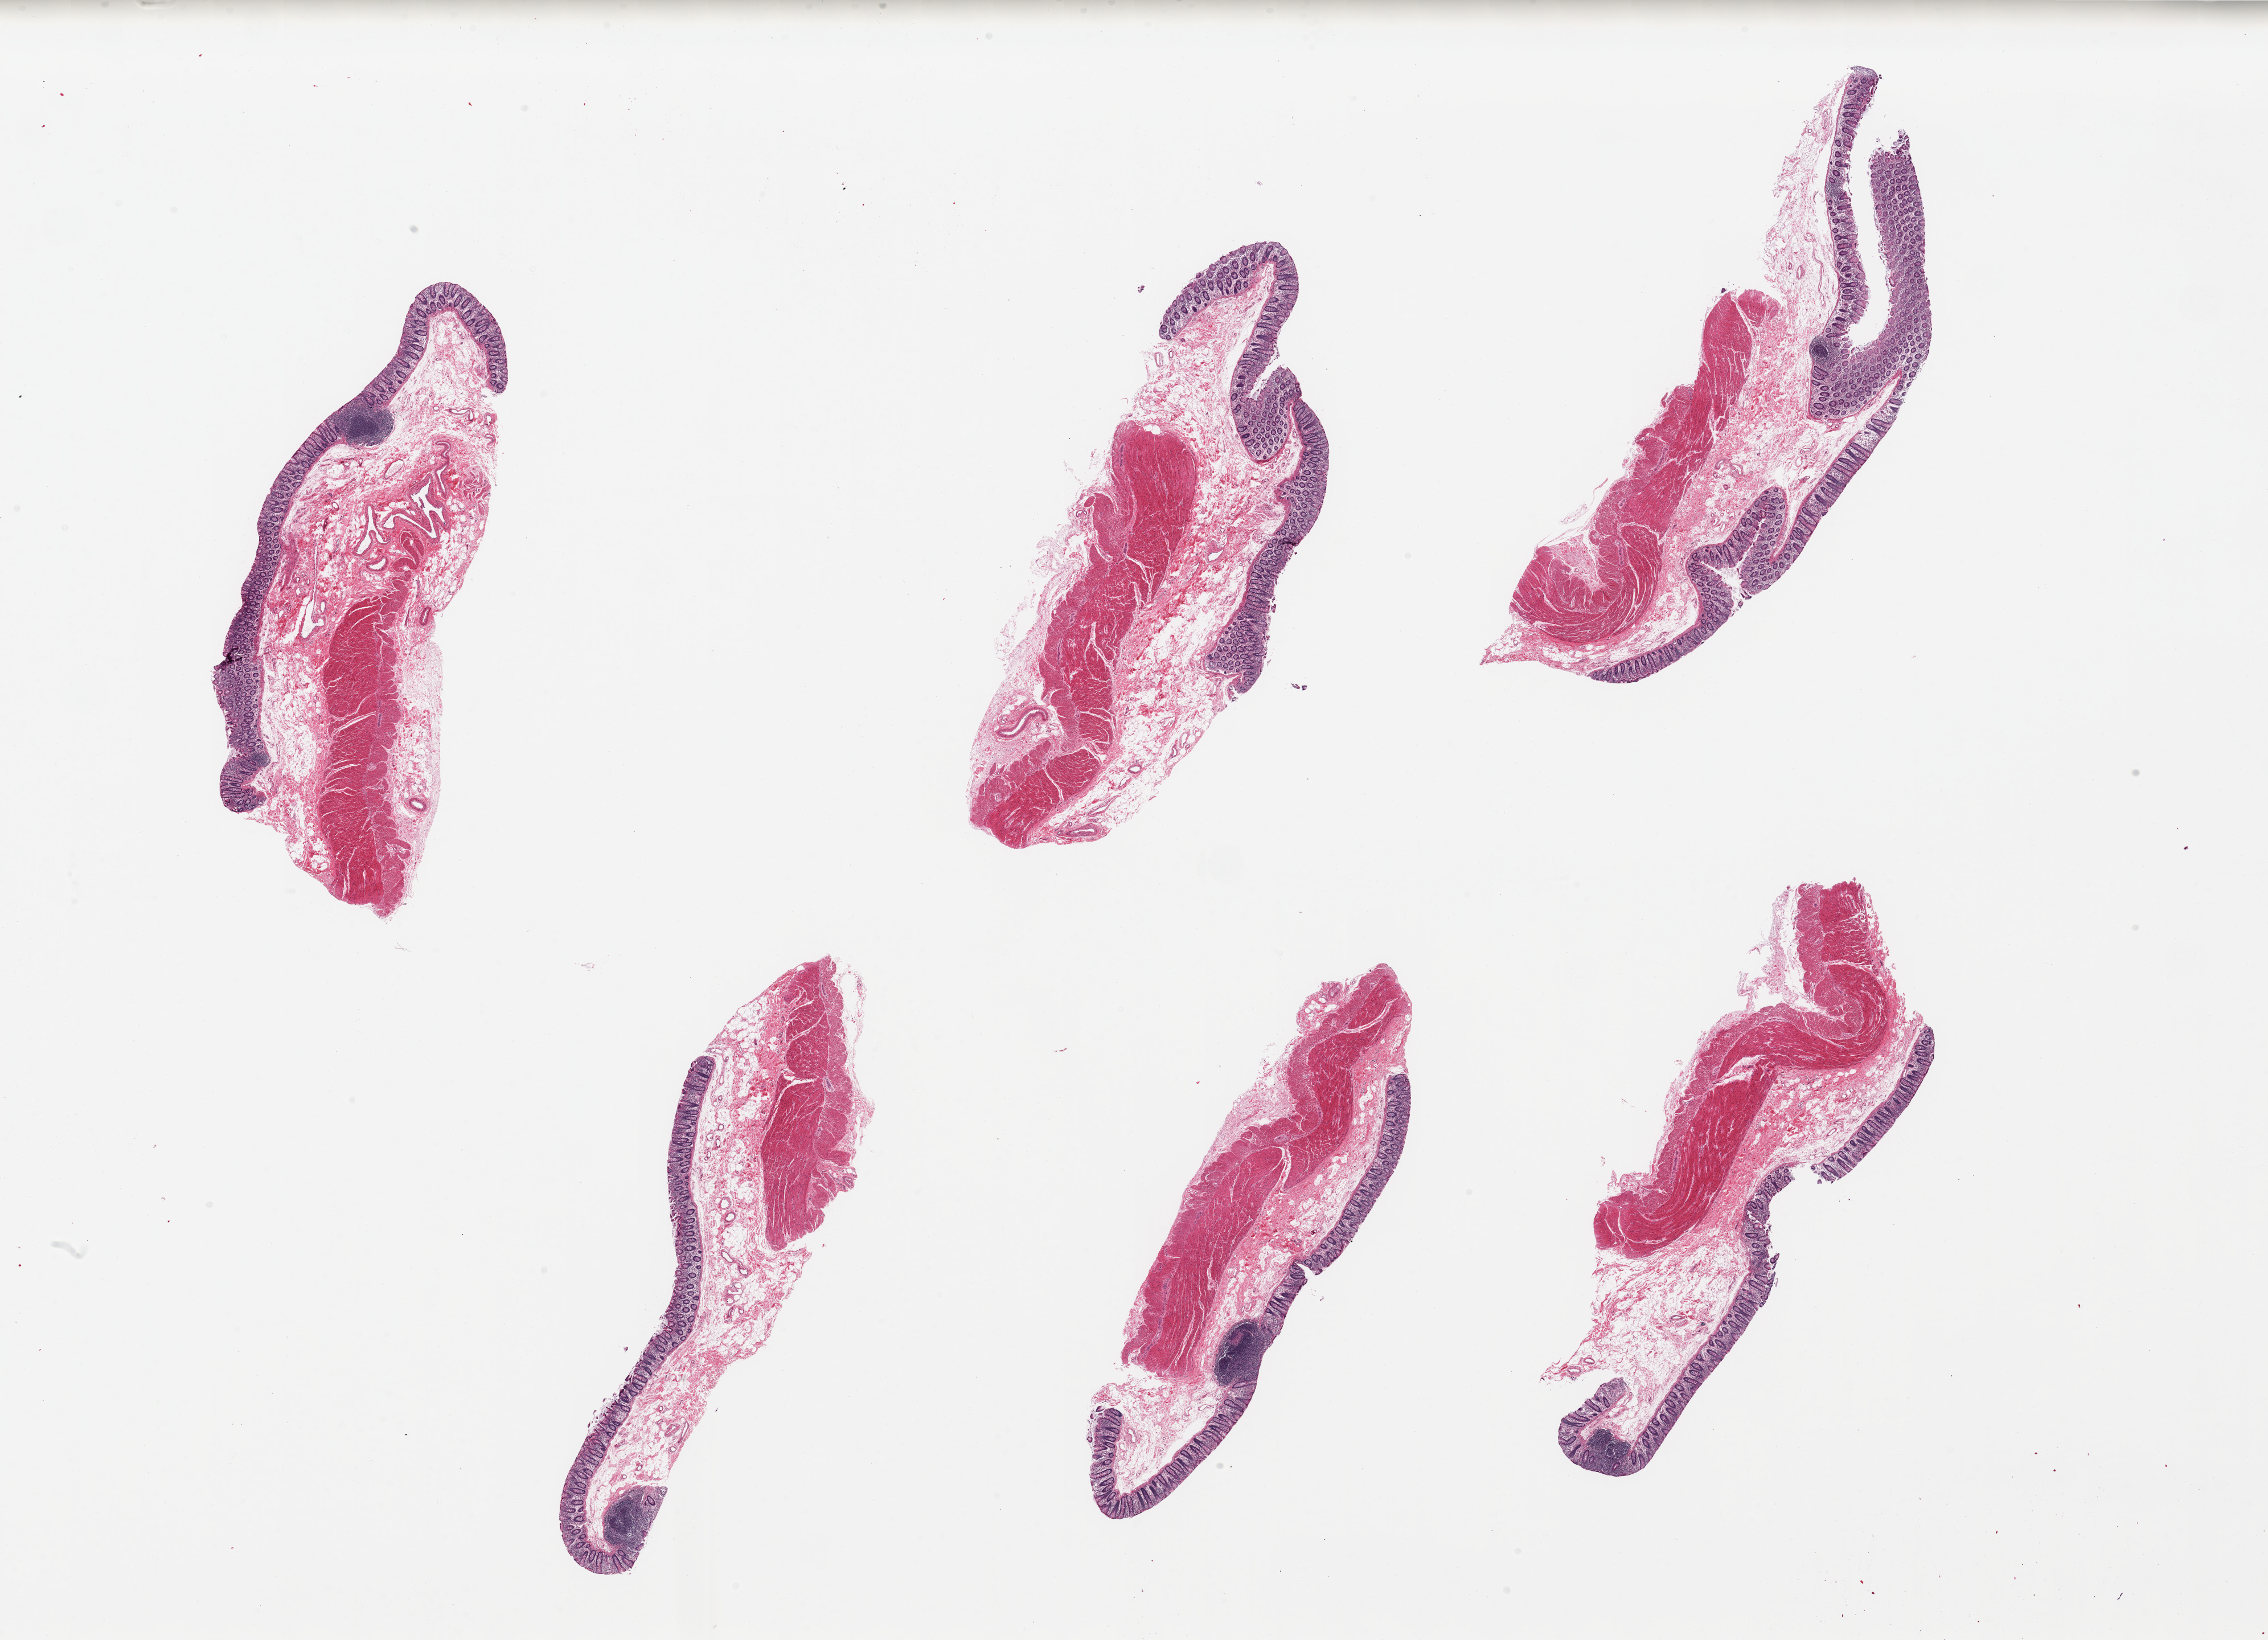
Whole-slide image, haematoxylin and eosin stain — a low-resolution overview of the entire scanned area, about 31.5 x 22.8 mm (slide scanned at 20x), PAXgene-fixed, paraffin-embedded tissue, target tissue: transverse colon, tissue donor sample. Donor: female.
Review note (as recorded): 6 pieces; full thickness sections.